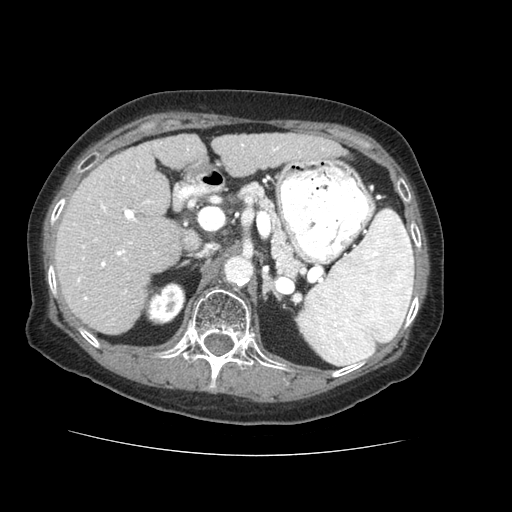
Contrast-enhanced abdominal CT (liver protocol), one axial slice; 120 kVp; soft-tissue window (W 400 / L 40 HU); 512 × 512 image matrix, field of view 360 × 360 mm. From the clinical record (not read from this slice): diagnosis: hepatocellular carcinoma (patient treated with transarterial chemoembolisation; whether this scan precedes or follows treatment is not stated here); TNM stage (as recorded): Stage-IVB; Child-Pugh class: A; tumour differentiation: well differentiated; tumour nodularity: uninodular.
Annotated regions visible in this slice (semi-automatically segmented with operator editing):
- liver parenchyma outside the tumour (the mass and vessels are separate outlines, so this box may not span the whole liver): box from (x=54, y=134) to (x=340, y=334) px
- liver vessels: (x=71, y=144)–(x=313, y=300)